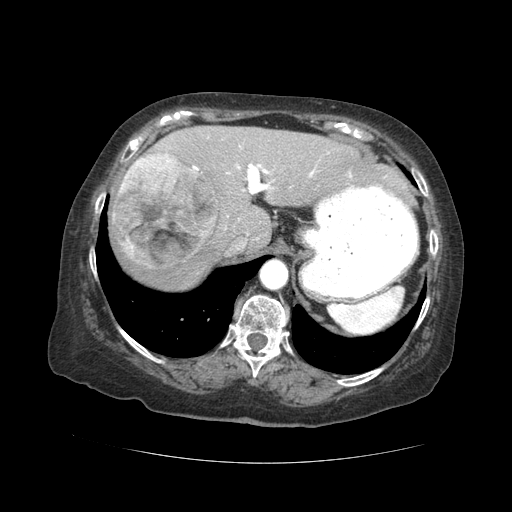
Contrast-enhanced abdominal CT (liver protocol), one axial slice; slice 33 of 59 in the series (ordered by position); reconstruction kernel STANDARD; 120 kVp; soft-tissue window (W 400 / L 40 HU); 2.5 mm slice thickness; 512 × 512 image matrix. From the clinical record (not read from this slice): diagnosis: hepatocellular carcinoma (patient treated with transarterial chemoembolisation; whether this scan precedes or follows treatment is not stated here); TNM stage (as recorded): Stage-I; Child-Pugh class: A.
Structures marked on this image (semi-automatic segmentation, software-assisted and operator-edited):
- abdominal aorta: box from (x=261, y=261) to (x=287, y=290) px
- liver parenchyma outside the tumour (the mass and vessels are separate outlines, so this box may not span the whole liver): (x=108, y=126)–(x=406, y=290)
- mass: (x=114, y=153)–(x=219, y=270)
- liver vessels: (x=192, y=145)–(x=386, y=229)